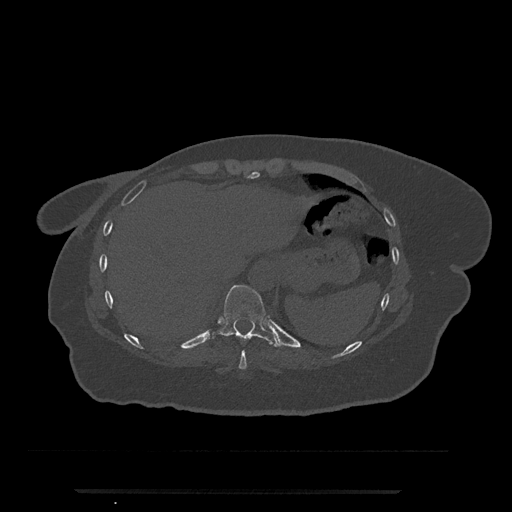
CT including the spine, one axial slice. Position 301 of 797 along the scan axis. Bone window (W 1800 / L 400 HU). 0.5 mm slice thickness. 512 × 512 image matrix. Female patient, age 51 years. Case-level facts recorded for this patient, not image findings: primary cancer: neuro; vertebrae with lytic lesions (as recorded): T8.
Annotated regions visible in this slice (semi-automatic segmentation, software-assisted and operator-edited):
- T10 vertebra: bounding box (x1, y1, x2, y2) in pixels: (213, 285, 278, 347)
- T9 vertebra: (239, 350, 247, 370)